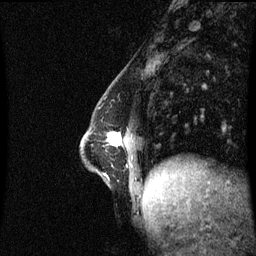
Breast MRI (dynamic contrast-enhanced), one sagittal slice. Position 22 of 60 along the scan axis. Dynamic contrast-enhanced series, image 2 of 3 at this slice position (ordered by acquisition). 1.5 T. TE 4.2 ms, TR 8.9 ms. 2.2 mm slice thickness. 256 × 256 image matrix, field of view 210 × 210 mm. Patient: female, 47 years. From the clinical record (not read from this slice): setting: breast cancer imaged before/during neoadjuvant chemotherapy; receptor status: HR-positive, HER2-negative.
Structures marked on this image (semi-automatically segmented with operator editing):
- analysis volume of interest (the breast-tissue region the enhancement analysis was run in; not a lesion): bounding box <82,132,142,193> (left, top, right, bottom; pixels)
- tumour enhancement mask (voxels above the 70 % enhancement threshold inside the analysis volume of interest): <110,133,121,146>